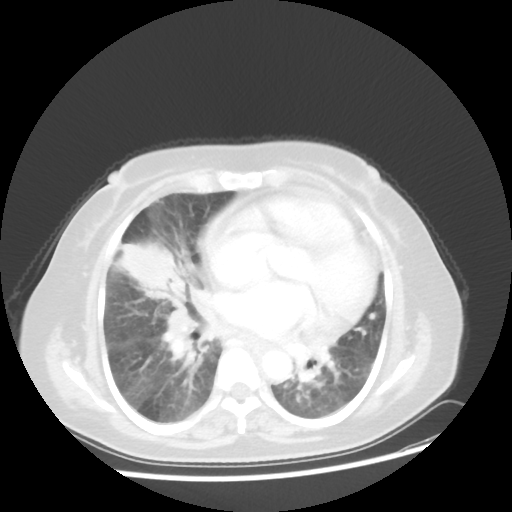
Chest CT, one axial slice. Position 21 of 45 along the scan axis. Reconstruction kernel STANDARD. Lung window (W 1500 / L -600 HU). 5 mm slice thickness. 512 × 512 image matrix. Female patient, age 67 years. Case-level facts recorded for this patient, not image findings: clinical TNM (as recorded): T2a N3 M1a.
Annotated regions visible in this slice (bounding box drawn by a radiologist):
- lung tumour (recorded histology: adenocarcinoma): bounding box <121,238,187,302> (left, top, right, bottom; pixels)